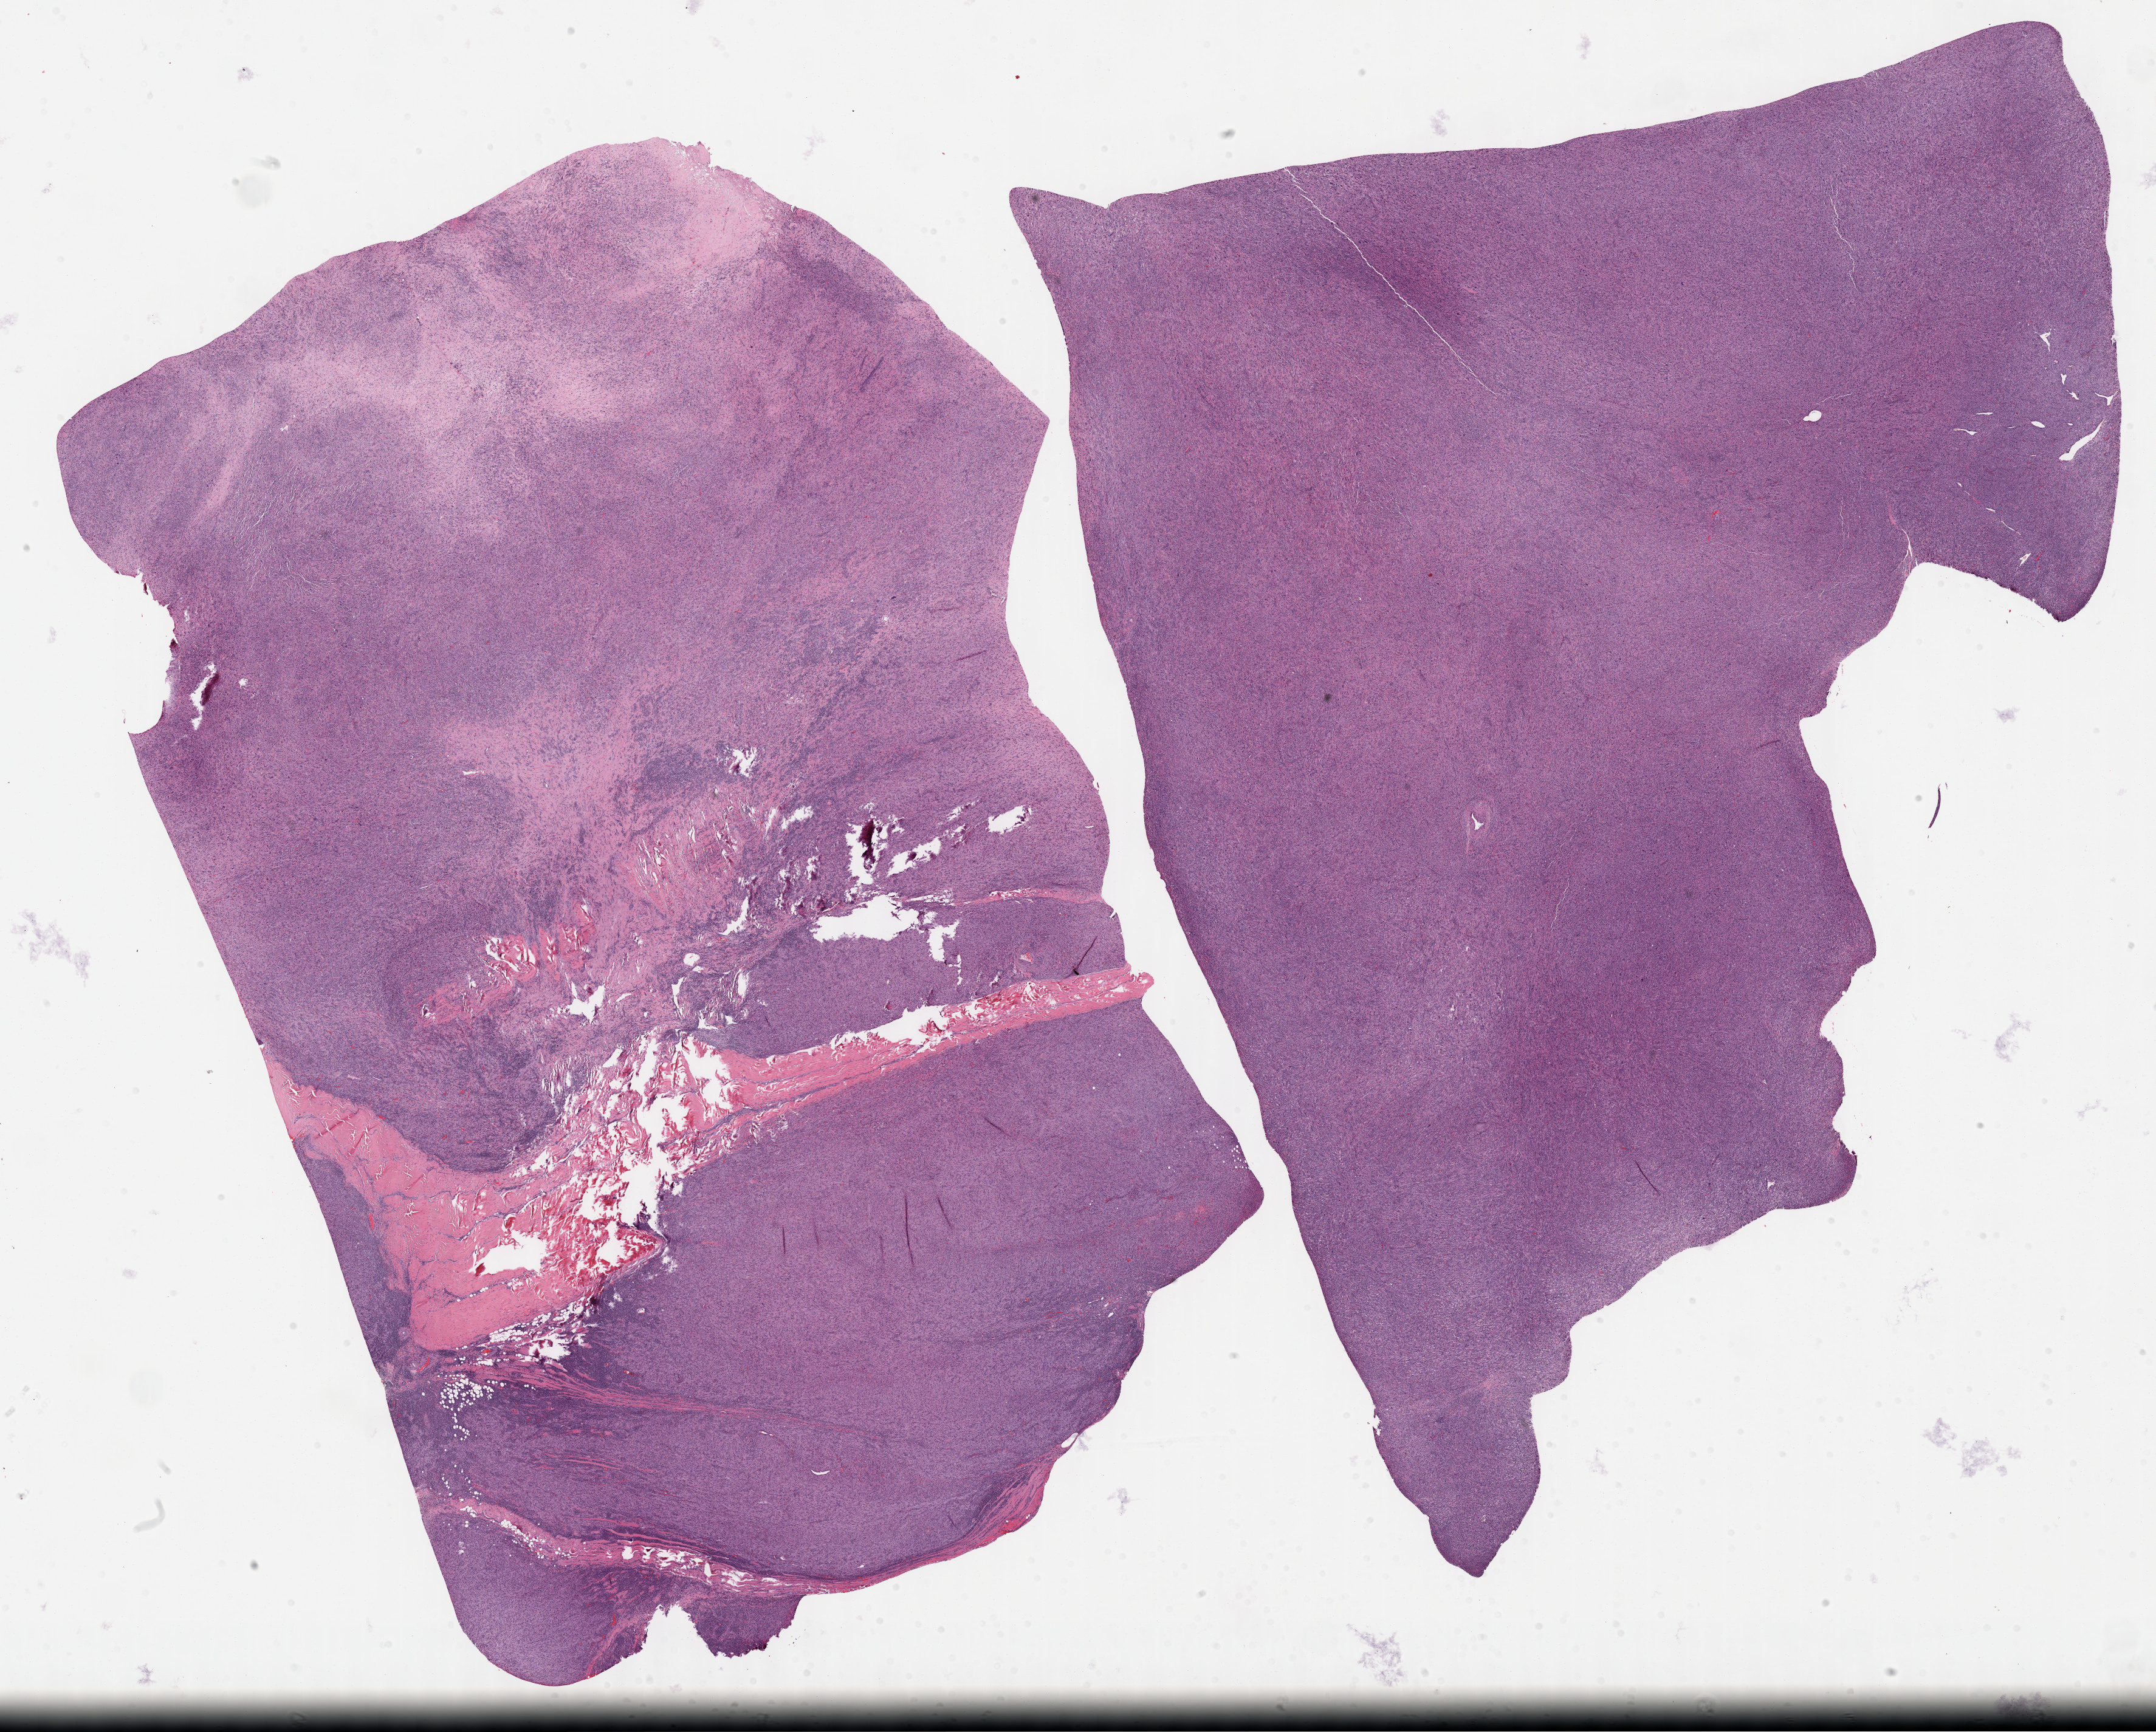
Whole-slide histology image, Hematoxylin and eosin (H&E) stained — a low-resolution overview of the entire scanned area, about 28.7 x 23.1 mm (from a 40x scan); formalin-fixed paraffin-embedded (FFPE) diagnostic section; connective, subcutaneous and other soft tissues, primary tumour sample. Female patient.
Pathologic diagnosis: Malignant fibrous histiocytoma (connective, subcutaneous and other soft tissues of trunk, NOS).